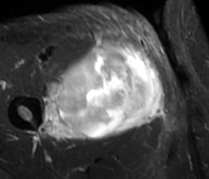
MRI of an extremity soft-tissue mass, one axial slice; slice 42 of 89 in the series (ordered by position); STIR; MR volume resampled by the dataset authors to the PET/CT grid (not the native acquisition matrix); 3.27 mm slice thickness; 209 × 179 image matrix. Male patient. From the clinical record (not read from this slice): histological type: undifferentiated - pleiomorphic; grade: high; site of the primary tumour: right thigh.
Annotated regions visible in this slice (expert contour drawn on MRI and transferred to this co-registered scan by the dataset authors):
- gross tumour volume including surrounding oedema: bounding box [x1, y1, x2, y2] px = [39, 41, 165, 141]
- gross tumour volume (mass): [55, 43, 163, 138]